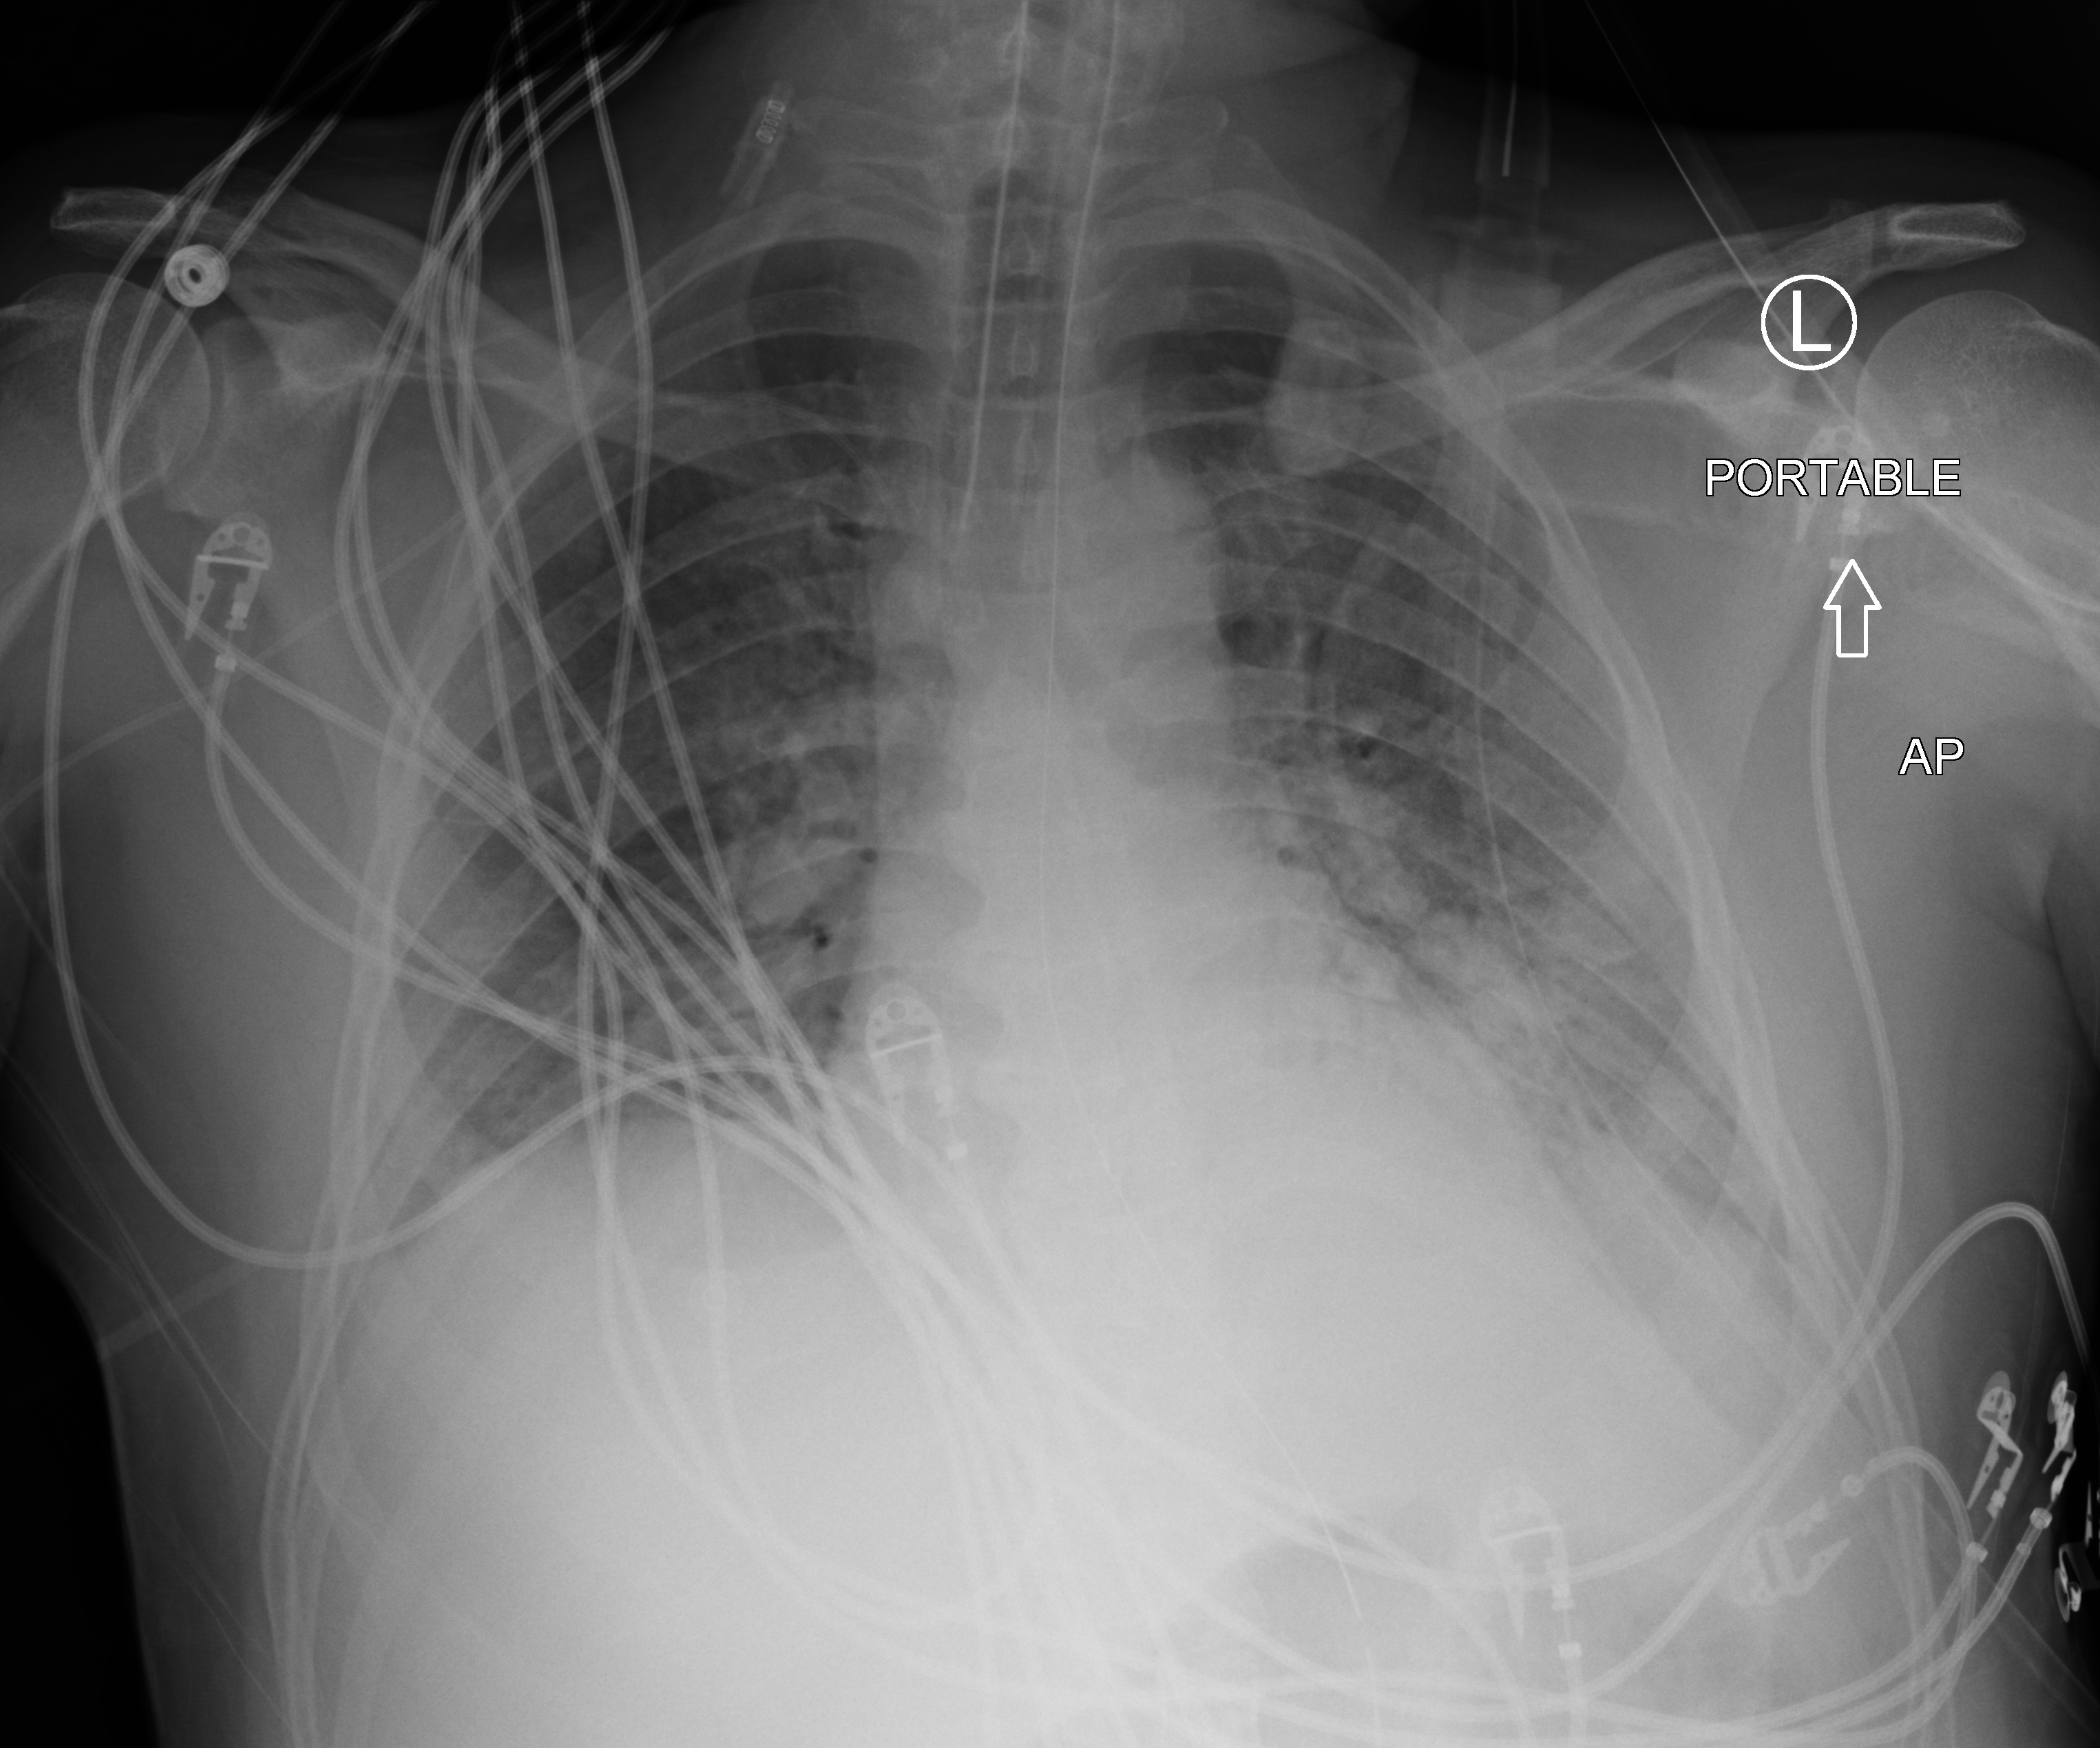
Portable chest radiograph, anteroposterior (AP) projection. Male patient hospitalised with COVID-19, age 18–59 years.
From the hospital-stay record, not from the radiograph (when in the stay this image was taken is not recorded):
- admitted to intensive care during this hospital stay: yes